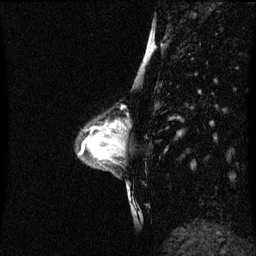
Breast MRI (dynamic contrast-enhanced), one sagittal slice. Position 25 of 60 along the scan axis. Dynamic contrast-enhanced series, image 2 of 3 at this slice position (ordered by acquisition). 1.5 T. TE 4.2 ms, TR 8.9 ms. 2 mm slice thickness. 256 × 256 image matrix, field of view 200 × 200 mm. Patient: female, 33 years. Case-level facts recorded for this patient, not image findings: setting: breast cancer imaged before/during neoadjuvant chemotherapy; receptor status: HER2-positive.
Outlined on this slice (semi-automatically segmented with operator editing):
- analysis volume of interest (the breast-tissue region the enhancement analysis was run in; not a lesion): bounding box (x1, y1, x2, y2) in pixels: (107, 116, 125, 147)
- tumour enhancement mask (voxels above the 70 % enhancement threshold inside the analysis volume of interest): (111, 126, 115, 127)